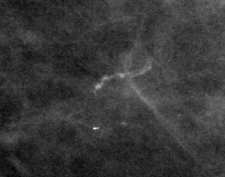
Region of interest cut from a scanned film mammogram (one marked finding); right breast; CC view.
Calcifications, morphology fine linear branching; BI-RADS assessment category 2; subtlety rating 4 on a 1 (subtle) to 5 (obvious) scale; benign; no additional work-up was recommended (benign without callback).